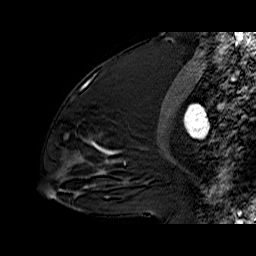
Breast MRI (dynamic contrast-enhanced), one sagittal slice. Slice 29 of 60 in the series (ordered by position). Dynamic contrast-enhanced series, time point 2 of 6 at this slice position (early post-contrast). 1.5 T. TE 6.3 ms, TR 32.9 ms. 4 mm slice thickness. 256 × 256 image matrix, field of view 200 × 200 mm. Female patient. Case-level facts recorded for this patient, not image findings: setting: breast cancer imaged before/during neoadjuvant chemotherapy; receptor status: triple-negative.
Annotated regions visible in this slice (semi-automatically segmented with operator editing):
- analysis volume of interest (the breast-tissue region the enhancement analysis was run in; not a lesion): bounding box (x1, y1, x2, y2) in pixels: (63, 77, 122, 170)
- tumour enhancement mask (voxels above the 100 % enhancement threshold inside the analysis volume of interest): (91, 142, 113, 162)